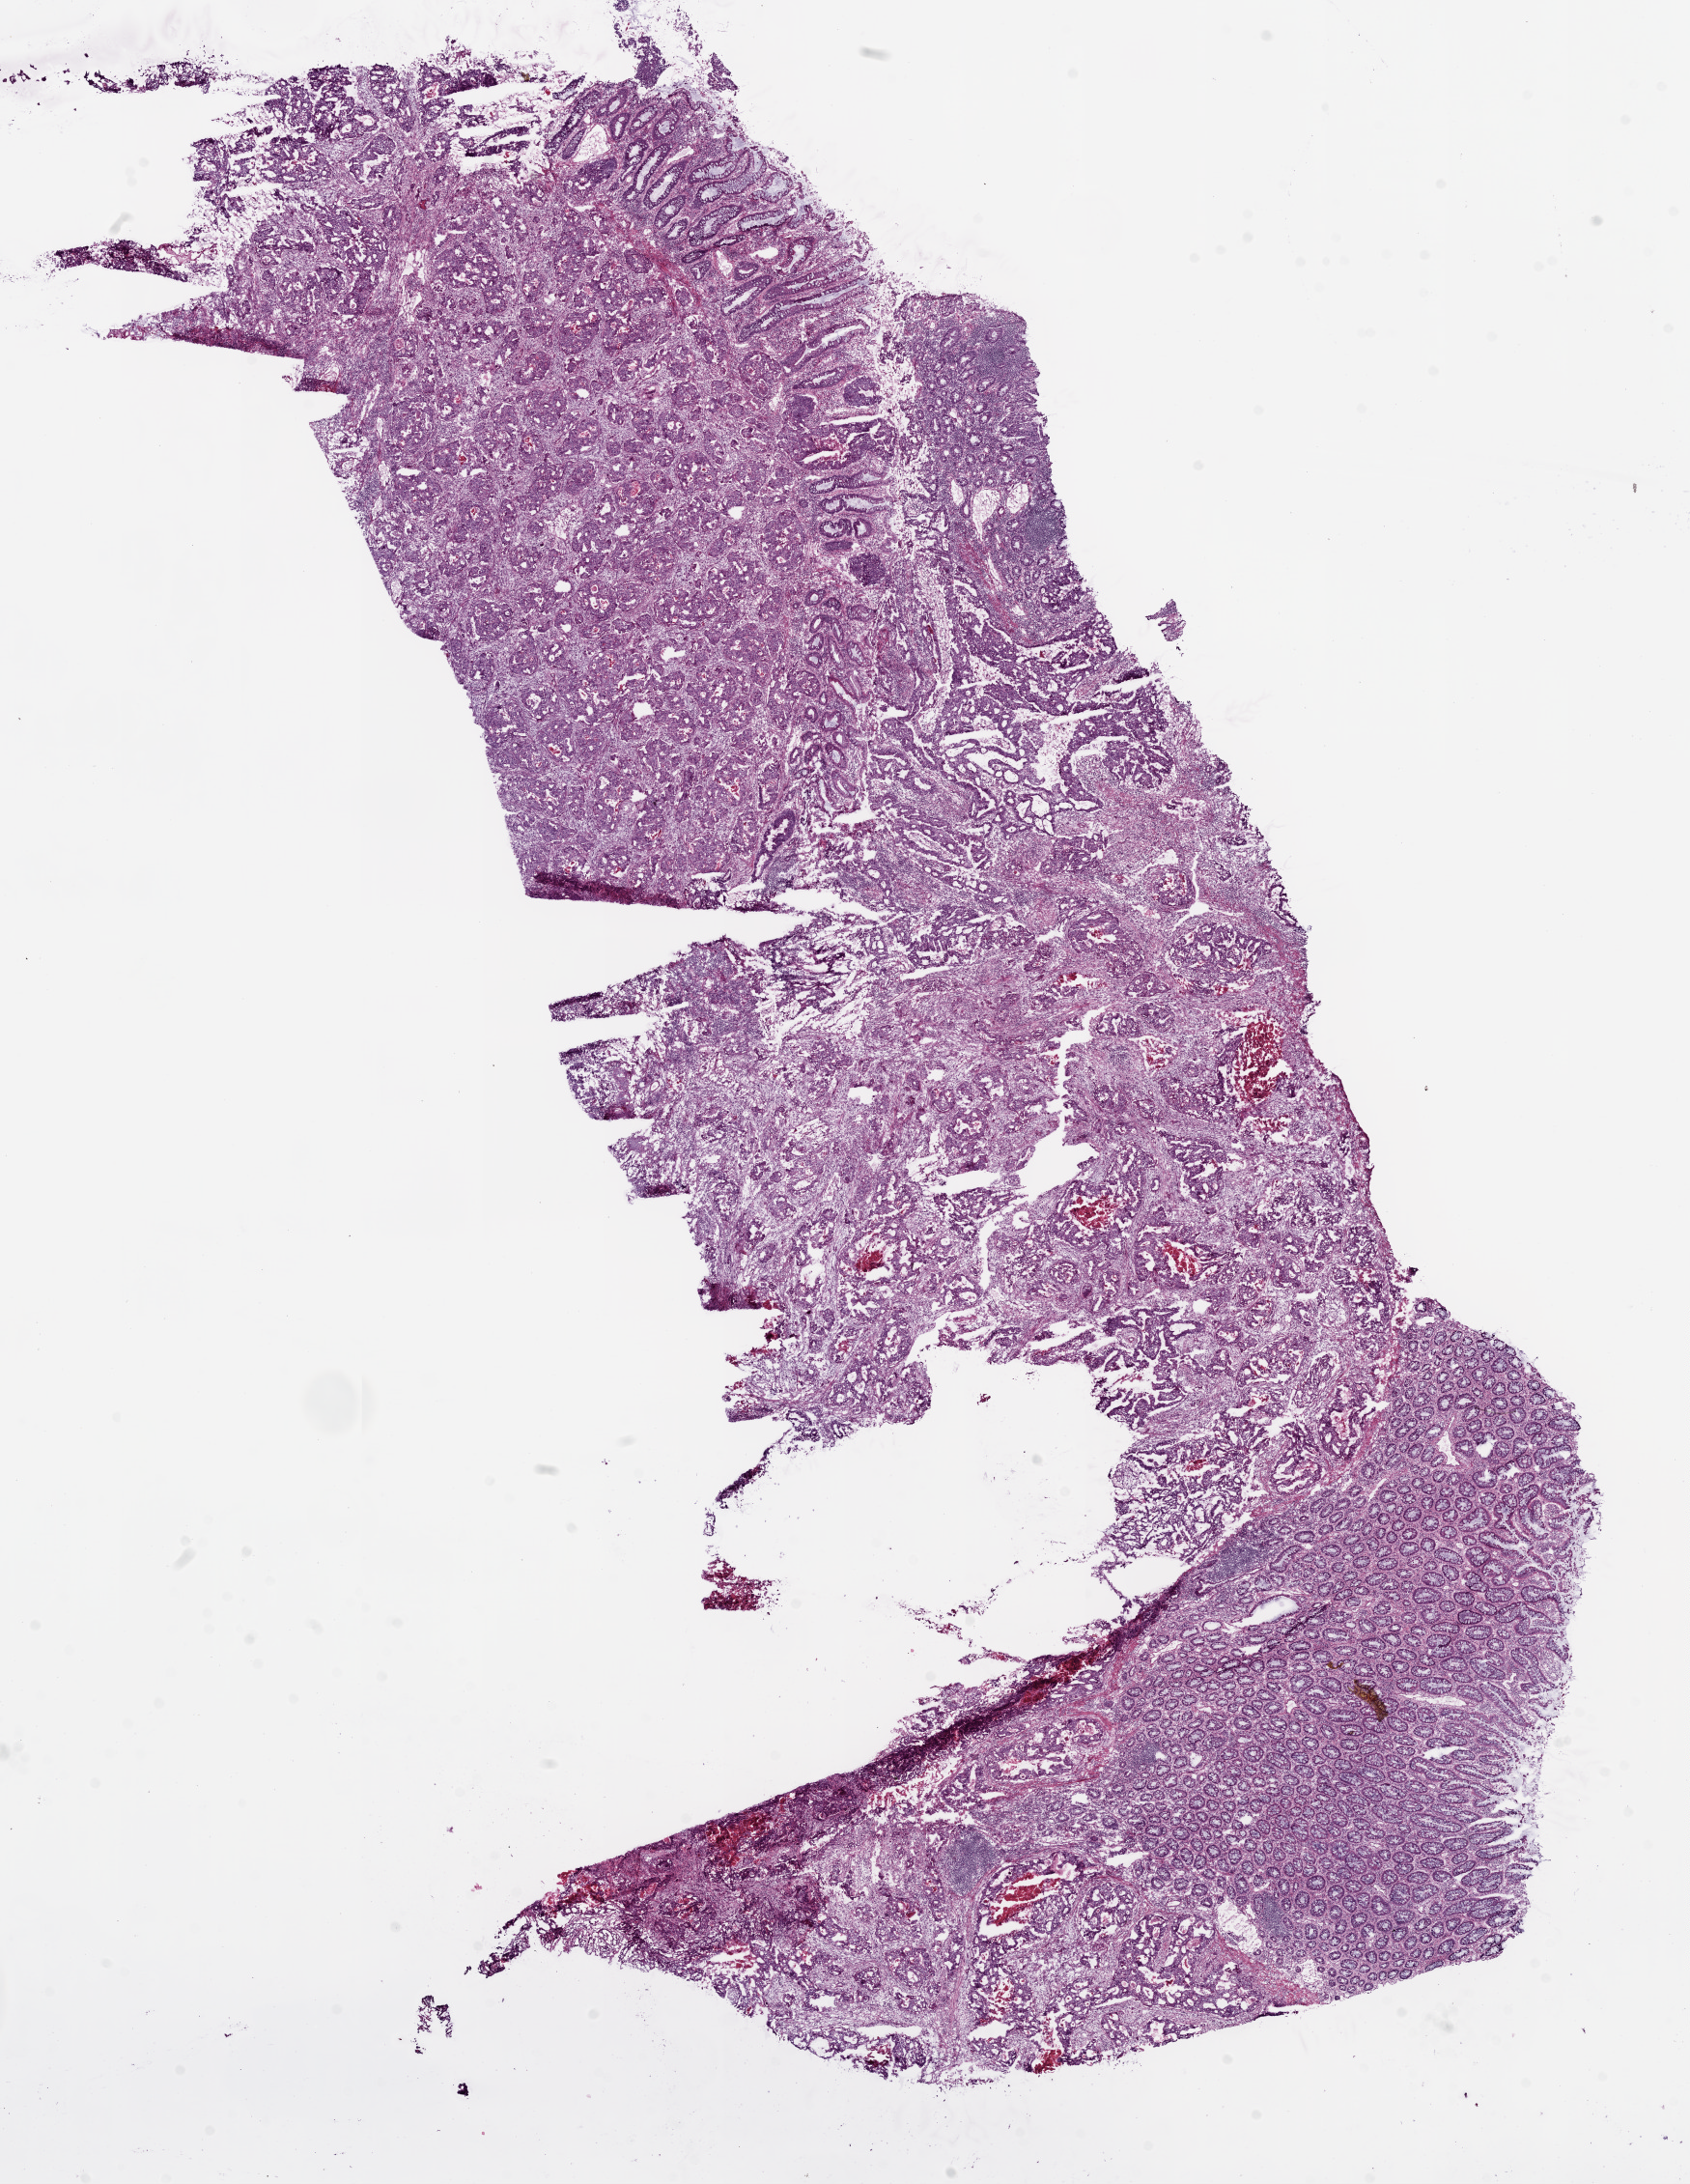
Whole-slide histology image, H&E-stained, a low-resolution overview of the entire scanned area, about 14.0 x 18.1 mm (from a 20x scan); frozen section from the bottom of the tissue portion; primary tumour sample from the colon. Male patient; age at initial diagnosis 49 years. Slide review estimates, as recorded: tumour cells 65%, tumour nuclei 75%.
Pathologic diagnosis: Adenocarcinoma, NOS.